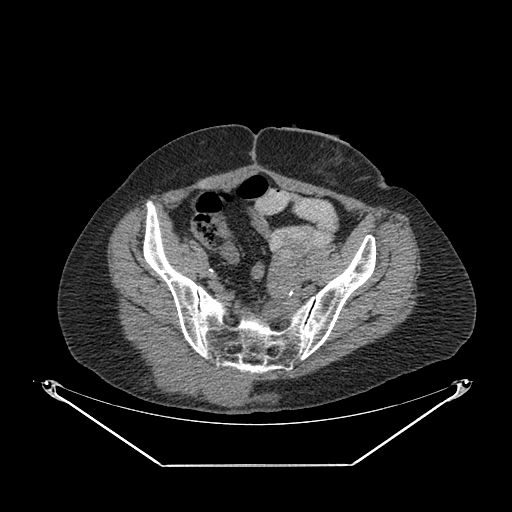
CT of an extremity soft-tissue mass (from a PET/CT study), one axial slice; position 71 of 267 along the scan axis; reconstruction kernel SOFT; 140 kVp; soft-tissue window (W 400 / L 40 HU); 3.75 mm slice thickness; 512 × 512 image matrix, field of view 500 × 500 mm. Female patient. From the clinical record (not read from this slice): histological type: spindle cell suggestive of myxofibrosarcoma; grade: intermediate; site of the primary tumour: right buttock.
Outlined on this slice (expert contour drawn on MRI and transferred to this co-registered scan by the dataset authors):
- gross tumour volume (mass): bounding box <135,345,250,407> (left, top, right, bottom; pixels)